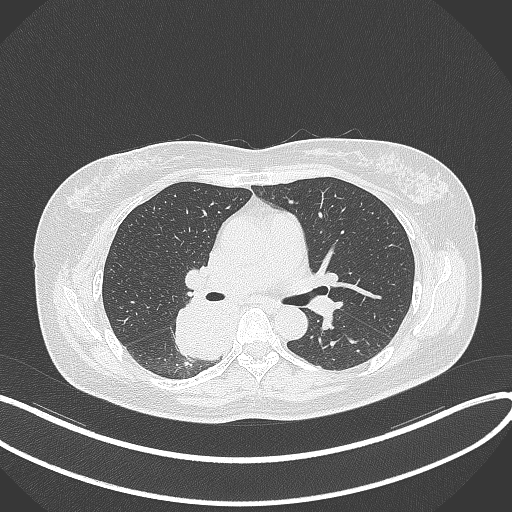
Chest CT, one axial slice. Position 212 of 331 along the scan axis. Reconstruction kernel B70f. Lung window (W 1500 / L -600 HU). 1 mm slice thickness. 512 × 512 image matrix, field of view 400 × 400 mm. Patient: female, 54 years. Case-level facts recorded for this patient, not image findings: clinical TNM (as recorded): T4 N0 M0.
Structures marked on this image (bounding box drawn by a radiologist):
- lung tumour (recorded histology: adenocarcinoma): bounding box <172,298,224,362> (left, top, right, bottom; pixels)